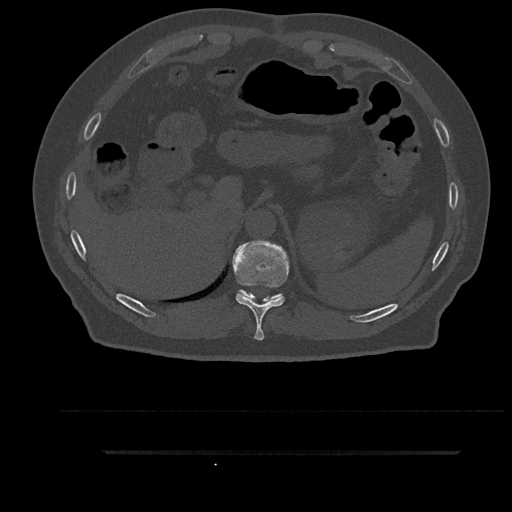
CT including the spine, one axial slice. Slice 346 of 797 in the series (ordered by position). Reconstruction kernel Br40s/3. 120 kVp. Bone window (W 1800 / L 400 HU). 512 × 512 image matrix. Male patient, age 63 years. Case-level facts recorded for this patient, not image findings: primary cancer: renal.
Structures marked on this image (semi-automatic segmentation, software-assisted and operator-edited):
- T10 vertebra: bounding box <232,241,289,341> (left, top, right, bottom; pixels)
- T11 vertebra: <238,290,282,301>